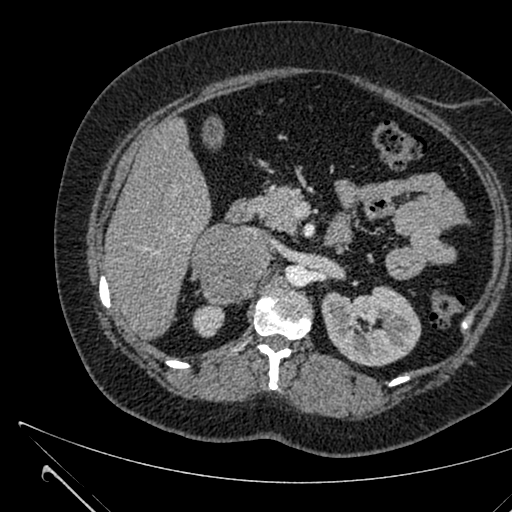
Contrast-enhanced abdominal CT, one axial slice. Position 386 of 731 along the scan axis. 120 kVp. Intravenous contrast given. Soft-tissue window (W 400 / L 40 HU). 1 mm slice thickness. 512 × 512 image matrix, field of view 376 × 376 mm. Patient: female, 36 years. From the clinical record (not read from this slice): diagnosis: adrenocortical carcinoma; tumour side: right adrenal; tumour size at pathology: 10 cm; Ki-67 index: 20 %; stage (as recorded): 4.
Outlined on this slice (semi-automatically segmented with operator editing):
- mass: bounding box <194,225,269,303> (left, top, right, bottom; pixels)